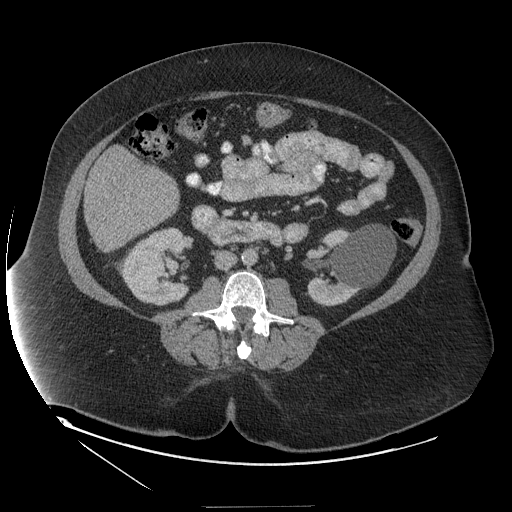
Contrast-enhanced abdominal CT (liver protocol), one axial slice. Position 38 of 127 along the scan axis. Reconstruction kernel STANDARD. 140 kVp. Soft-tissue window (W 400 / L 40 HU). 2.5 mm slice thickness. 512 × 512 image matrix, field of view 480 × 480 mm. Case-level facts recorded for this patient, not image findings: diagnosis: hepatocellular carcinoma (patient treated with transarterial chemoembolisation; whether this scan precedes or follows treatment is not stated here); TNM stage (as recorded): Stage-II; Child-Pugh class: A; tumour differentiation: well differentiated.
Outlined on this slice (semi-automatically segmented with operator editing):
- liver parenchyma outside the tumour (the mass and vessels are separate outlines, so this box may not span the whole liver): bounding box <84,152,178,252> (left, top, right, bottom; pixels)